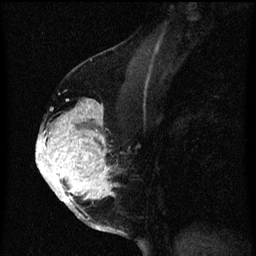
Breast MRI (dynamic contrast-enhanced), one sagittal slice. Position 35 of 60 along the scan axis. Dynamic contrast-enhanced series, image 2 of 3 at this slice position (ordered by acquisition). 1.5 T. TE 4.2 ms, TR 8 ms. 256 × 256 image matrix. Female patient, age 56 years.
Outlined on this slice (semi-automatic segmentation, software-assisted and operator-edited):
- analysis volume of interest (the breast-tissue region the enhancement analysis was run in; not a lesion): bounding box (x1, y1, x2, y2) in pixels: (40, 100, 123, 207)
- tumour enhancement mask (voxels above the 70 % enhancement threshold inside the analysis volume of interest): (40, 100, 117, 207)